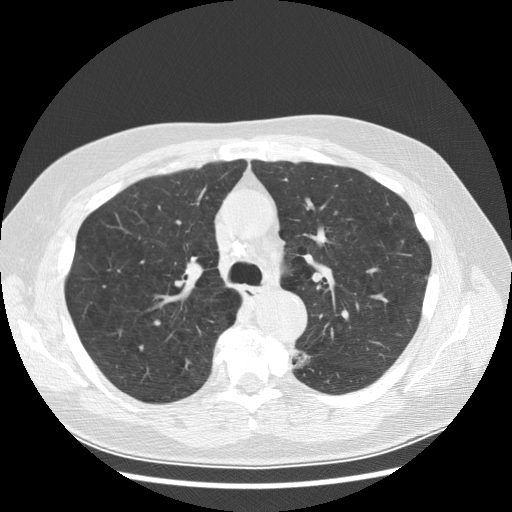
Low-dose screening chest CT, one axial slice. Slice 194 of 282 in the series (ordered by position). Reconstruction kernel STANDARD. 120 kVp. Lung window (W 1500 / L -600 HU). 2.5 mm slice thickness. 512 × 512 image matrix, field of view 370 × 370 mm.
Outlined on this slice (manually delineated by an expert):
- lesion 1 (tumor, lower lobe of left lung): box from (x=294, y=351) to (x=310, y=368) px